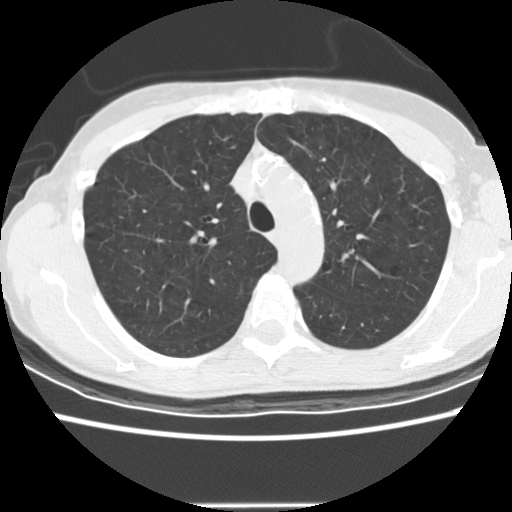
Chest CT (low-dose screening protocol), one axial image; second annual screen; lung window (W 1500 / L -600 HU); 2.5 mm slice thickness; slice 42 of 166 in the series. Female, age 58 years at enrolment.
• Expert reader's lesion annotation, bounding box [x1, y1, x2, y2] px = [170, 298, 214, 330].
• The screening reader recorded 2 non-calcified nodules or masses ≥4 mm on this exam; which of them this box marks is not recorded.
• Later outcome: lung cancer diagnosed 434 days after this screen — bronchiolo-alveolar adenocarcinoma, NOS, right upper lobe, well differentiated (G1), stage IA (AJCC 6th edition), 8 mm at pathology.